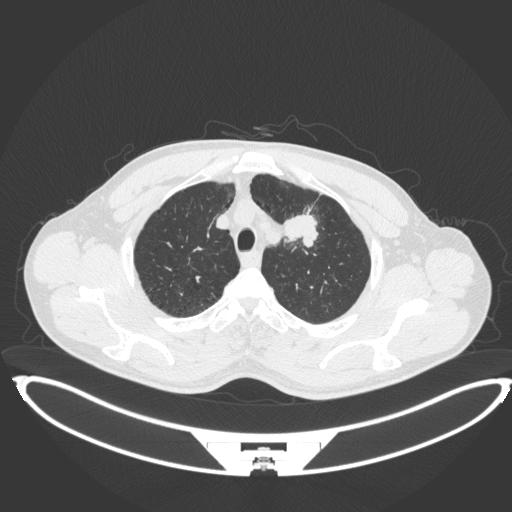
Chest CT, one axial slice. Slice 362 of 407 in the series (ordered by position). Lung window (W 1500 / L -600 HU). 512 × 512 image matrix. Male patient, age 60 years. From the clinical record (not read from this slice): clinical TNM (as recorded): T2a N0 M0; histopathological grade: G1-G2.
Annotated regions visible in this slice (bounding box drawn by a radiologist):
- lung tumour (recorded histology: squamous cell carcinoma): bounding box <281,213,319,248> (left, top, right, bottom; pixels)